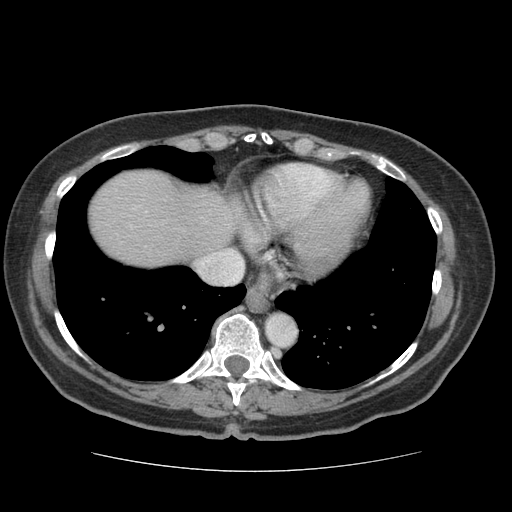
Contrast-enhanced abdominal CT (liver protocol), one axial slice. Slice 66 of 75 in the series (ordered by position). 140 kVp. Soft-tissue window (W 400 / L 40 HU). 2.5 mm slice thickness. 512 × 512 image matrix. From the clinical record (not read from this slice): diagnosis: hepatocellular carcinoma (patient treated with transarterial chemoembolisation; whether this scan precedes or follows treatment is not stated here); TNM stage (as recorded): Stage-I; Child-Pugh class: A.
Annotated regions visible in this slice (semi-automatically segmented with operator editing):
- liver parenchyma outside the tumour (the mass and vessels are separate outlines, so this box may not span the whole liver): box from (x=90, y=170) to (x=246, y=266) px